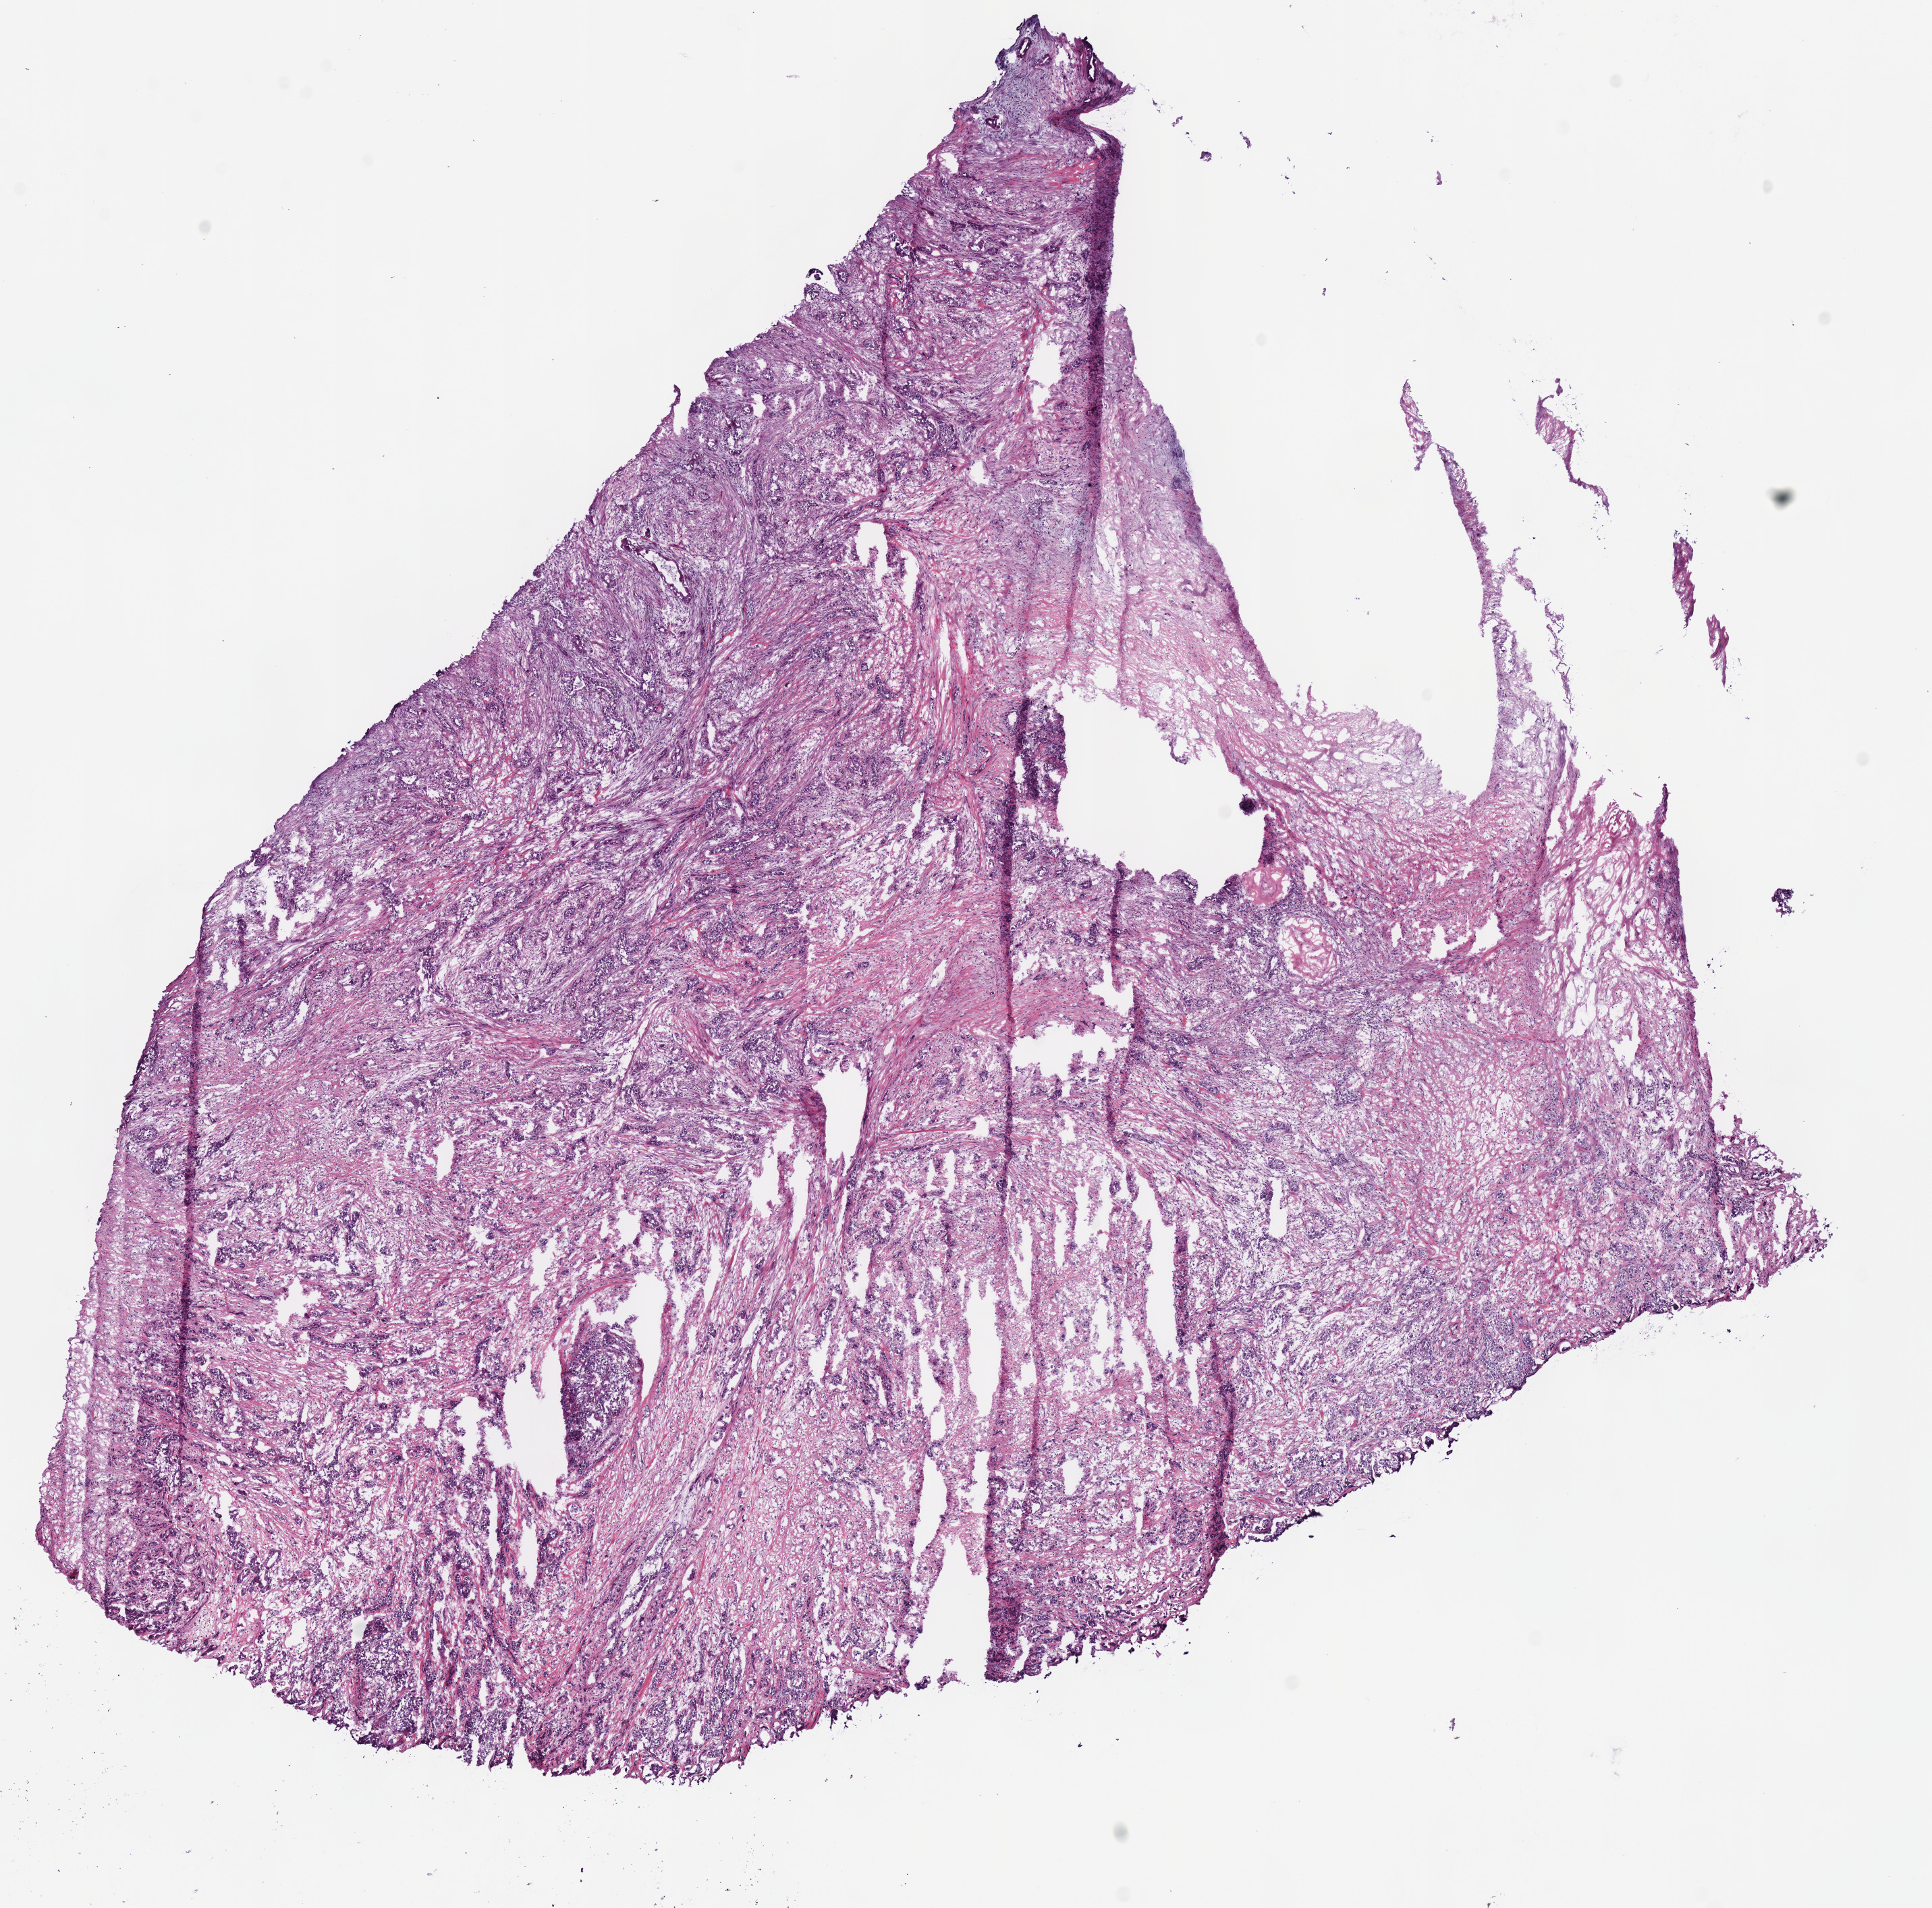
Digitized H&E tissue section (whole slide), low-resolution overview of the scanned area, about 11.3 x 11.1 mm (acquisition: 40x scan); frozen section from the bottom of the tissue portion; primary tumour sample from the pancreas. Patient: male, age at initial diagnosis 64 years. Pathologist review of this section (percent, as recorded): tumour cells 85%, tumour nuclei 75%.
Diagnosis: Infiltrating duct carcinoma, NOS.